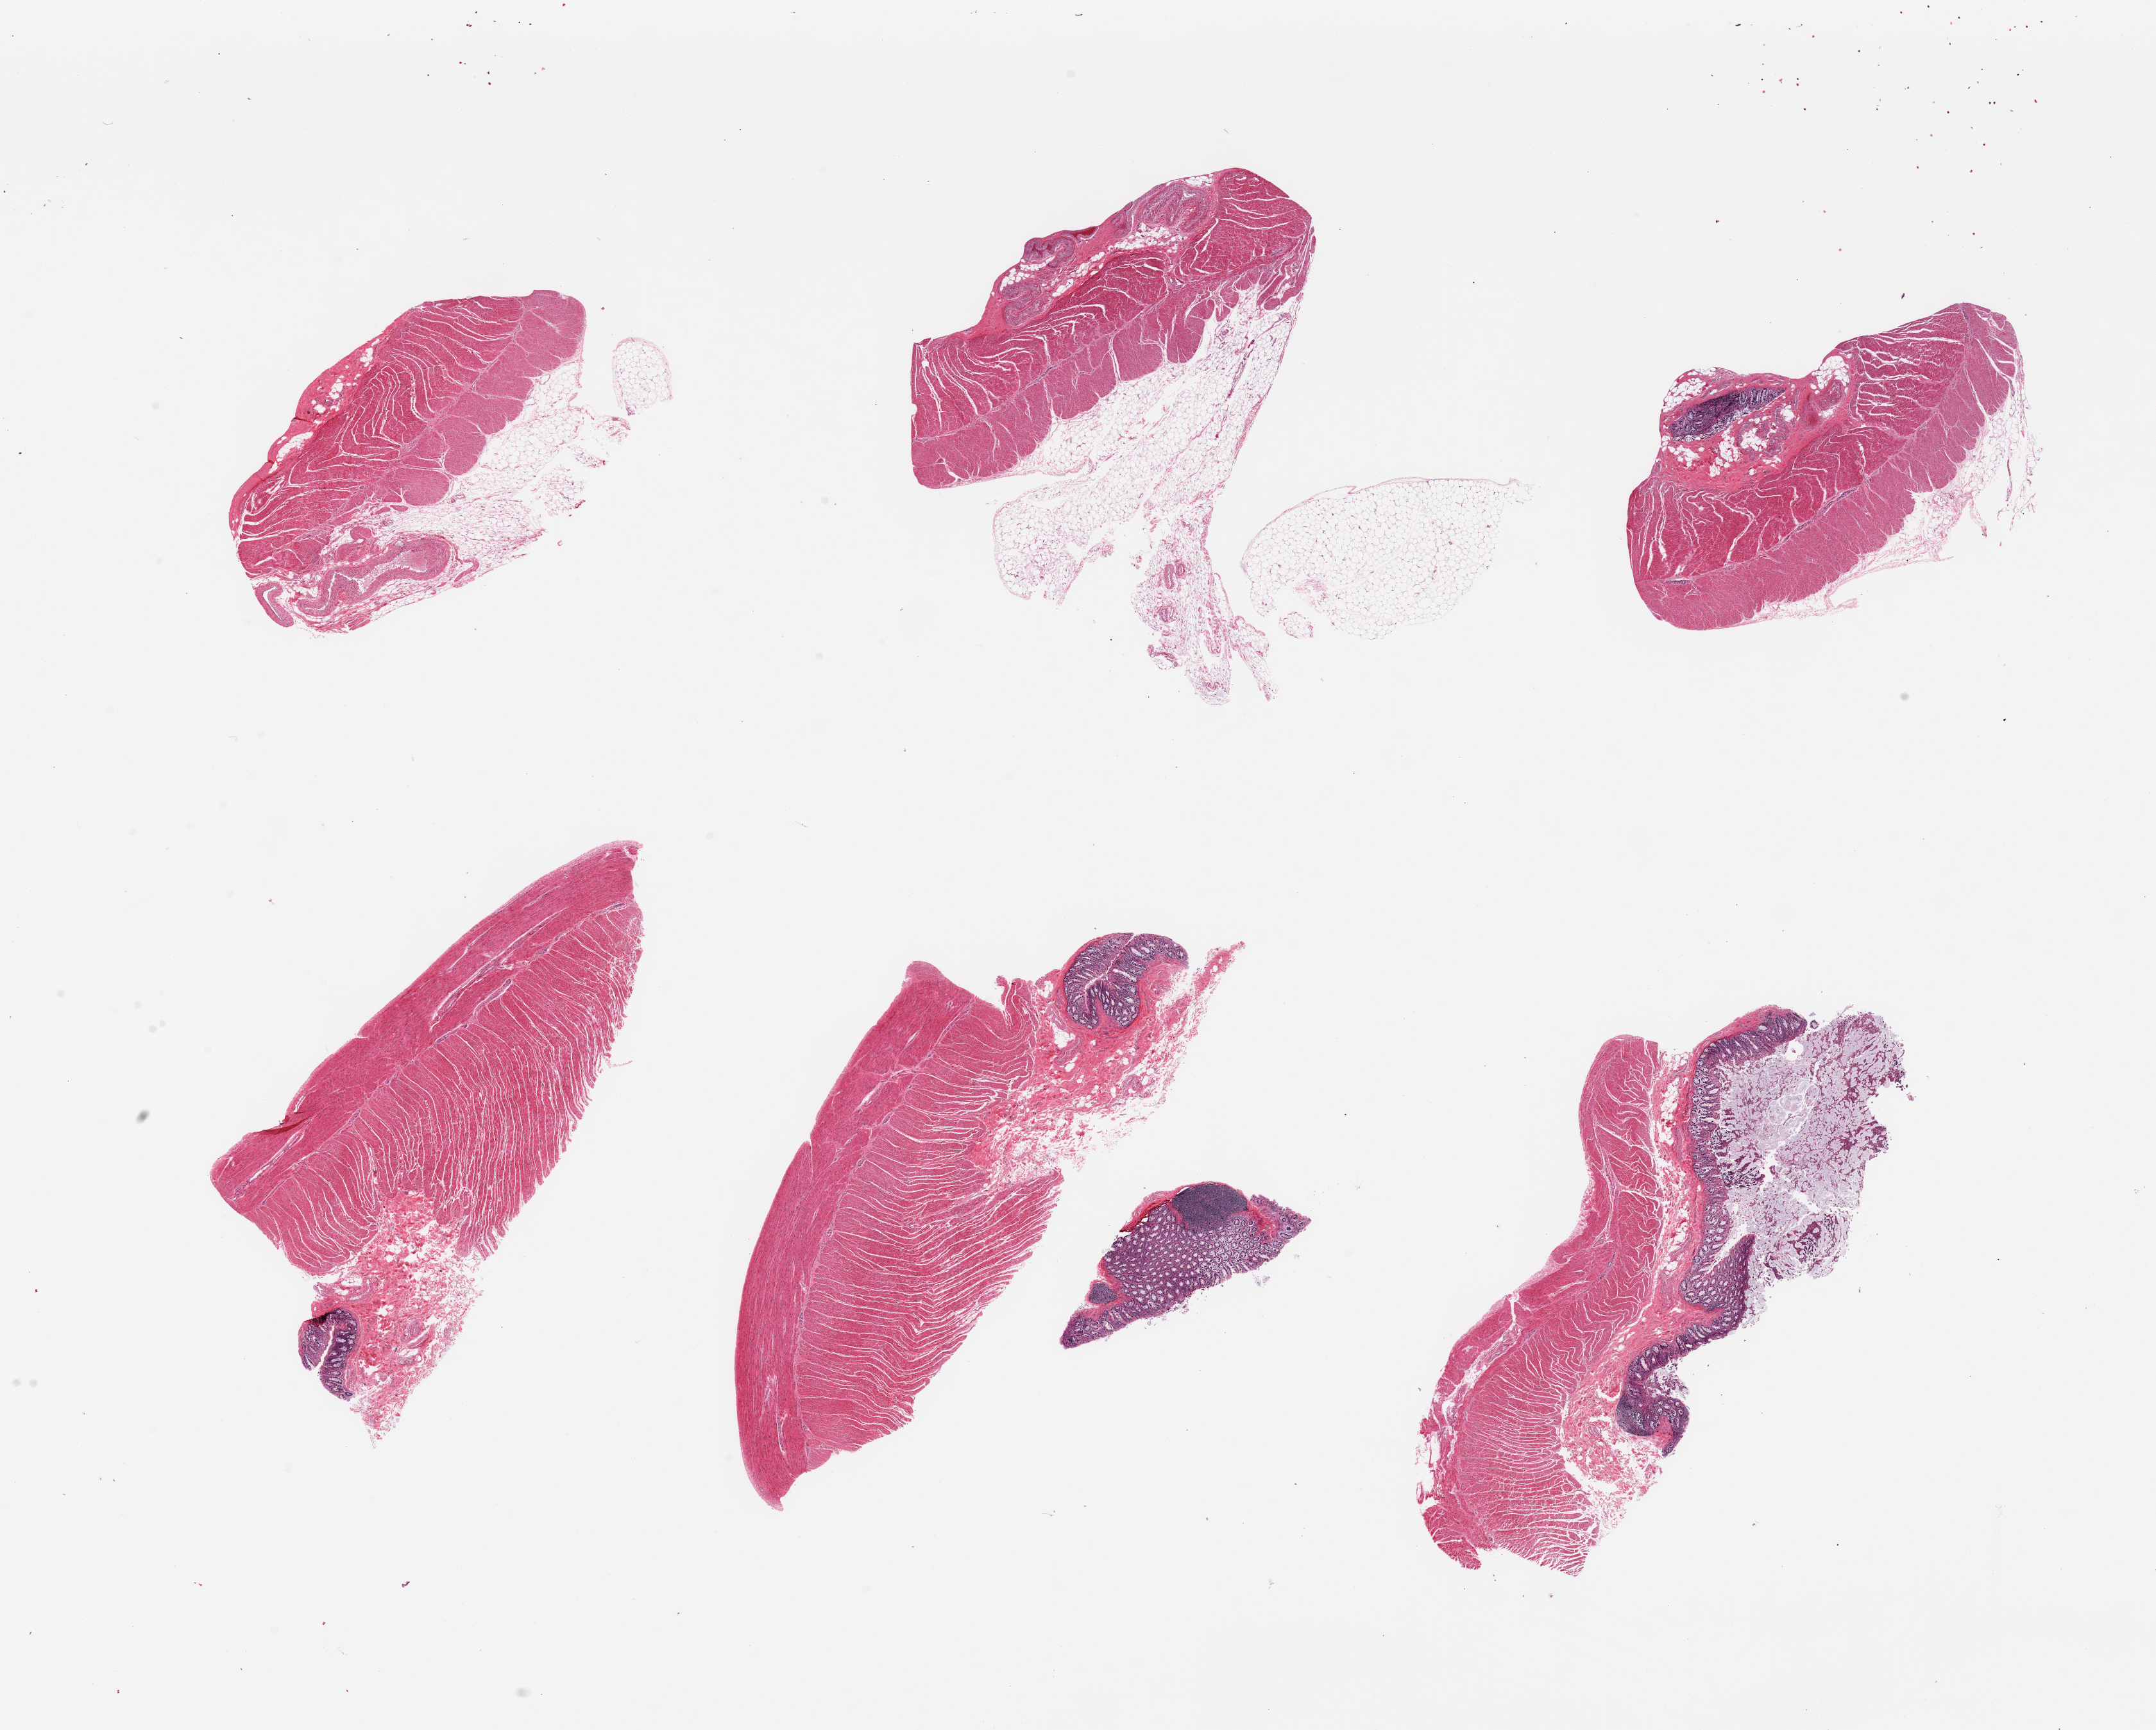
Hematoxylin and eosin (H&E) whole-slide image, low-resolution overview of the scanned area, about 26.6 x 21.3 mm (acquisition: 20x scan); PAXgene-fixed paraffin-embedded (PFPE) section; target tissue: transverse colon; tissue donor sample. Donor: male.
Pathologist's review note for this sample: 6 pieces; all have muscularis propria; minimal mucosa on 4.